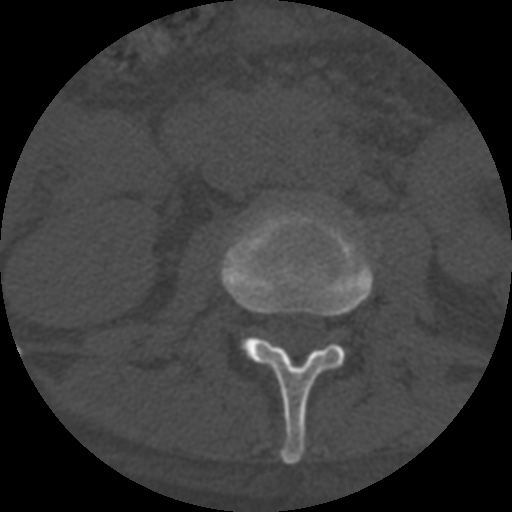
CT including the spine, one axial slice; slice 253 of 708 in the series (ordered by position); reconstruction kernel STANDARD; one of 3 acquisitions stored at this slice position; bone window (W 1800 / L 400 HU); 1.25 mm slice thickness; 512 × 512 image matrix. Patient age 55 years. Case-level facts recorded for this patient, not image findings: primary cancer: colon.
Outlined on this slice (semi-automatic segmentation, software-assisted and operator-edited):
- L2 vertebra: bounding box <220,204,380,465> (left, top, right, bottom; pixels)